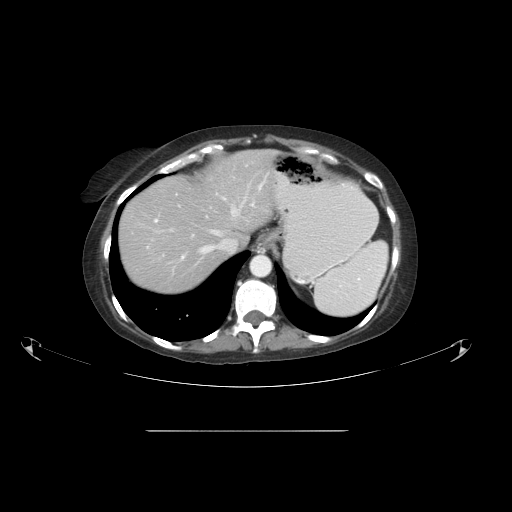
Contrast-enhanced abdominal CT, one axial slice. Slice 41 of 51 in the series (ordered by position). Reconstruction kernel STANDARD. 120 kVp. Intravenous contrast given. Soft-tissue window (W 400 / L 40 HU). 5 mm slice thickness. 512 × 512 image matrix, field of view 475 × 475 mm. Female patient, age 48 years. From the clinical record (not read from this slice): diagnosis: colorectal cancer liver metastases, imaged before liver resection; multiple liver metastases: yes; largest metastasis: 1 cm; chemotherapy before resection: no.
Outlined on this slice (expert manual segmentation):
- hepatic veins: bounding box [x1, y1, x2, y2] px = [200, 176, 266, 254]
- liver: [118, 151, 276, 295]
- planned liver remnant (the part of the liver to remain after resection): [118, 176, 231, 295]
- portal vein (with intrahepatic branches): [147, 193, 217, 260]